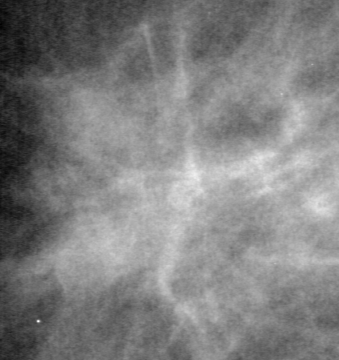
Region of interest cut from a scanned film mammogram (one marked finding); left breast; CC view; BI-RADS breast density category 2 (scale 1–4).
Finding: mass, shape irregular, margins spiculated; BI-RADS assessment category 5; pathology result (as recorded, not read from the image): malignant.